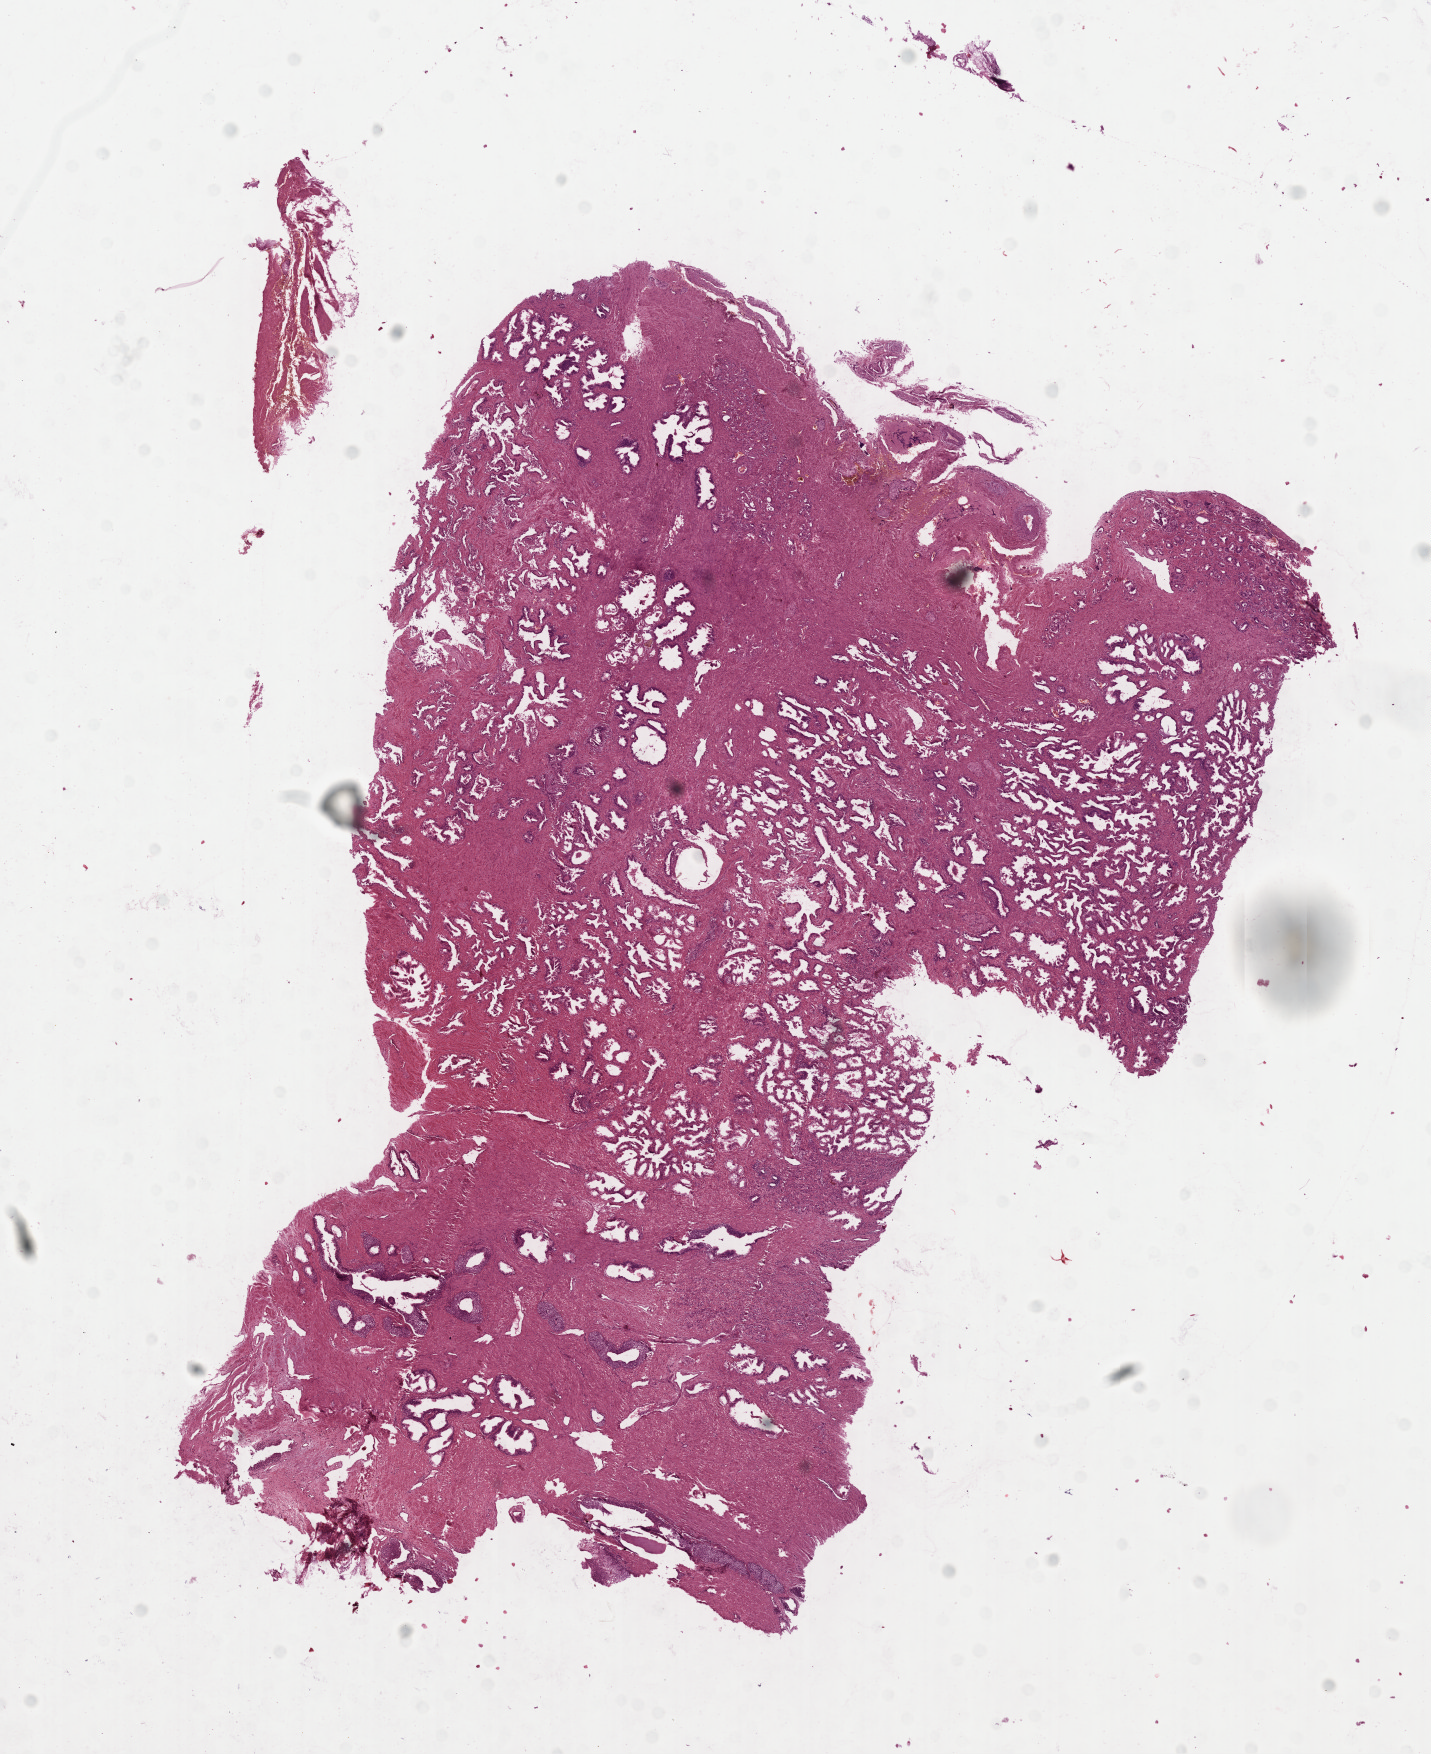
Whole-slide histology image, Hematoxylin and eosin (H&E) stained, a low-resolution overview of the entire scanned area, about 11.6 x 14.2 mm; formalin-fixed paraffin-embedded (FFPE) diagnostic section; prostate, primary tumour sample. Male patient; age at initial diagnosis 60 years. Gleason score: 8 (5+3).
Diagnosis: Adenocarcinoma, NOS (prostate gland). Laterality: right.